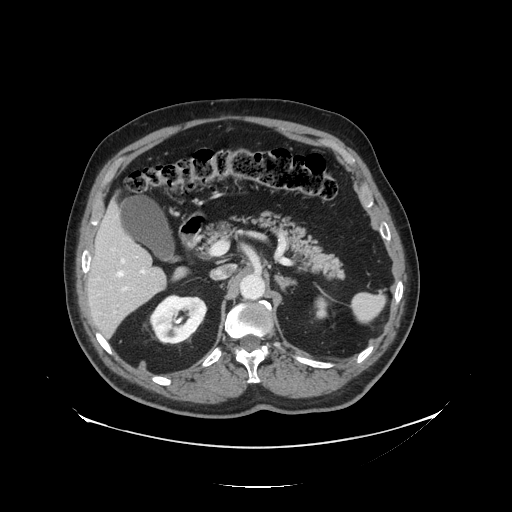
Contrast-enhanced abdominal CT, one axial slice; slice 74 of 138 in the series (ordered by position); reconstruction kernel STANDARD; intravenous contrast given; soft-tissue window (W 400 / L 40 HU); 2.5 mm slice thickness; 512 × 512 image matrix, field of view 497 × 497 mm. Male patient, age 77 years. From the clinical record (not read from this slice): diagnosis: colorectal cancer liver metastases, imaged before liver resection; multiple liver metastases: no; largest metastasis: 1.5 cm.
Structures marked on this image (outlined manually by an expert reader):
- hepatic veins: box from (x=117, y=259) to (x=125, y=277) px
- liver: (x=86, y=206)–(x=168, y=337)
- planned liver remnant (the part of the liver to remain after resection): (x=87, y=206)–(x=154, y=287)
- portal vein (with intrahepatic branches): (x=121, y=269)–(x=146, y=291)
- liver metastasis: (x=161, y=286)–(x=165, y=290)